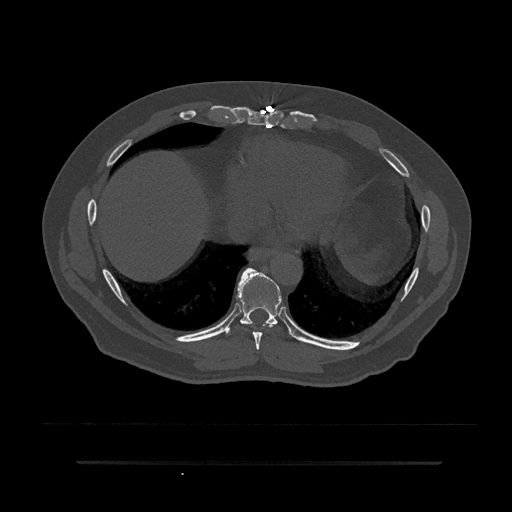
CT including the spine, one axial slice. Slice 399 of 797 in the series (ordered by position). Reconstruction kernel Br40s/3. Bone window (W 1800 / L 400 HU). 0.5 mm slice thickness. 512 × 512 image matrix. Patient: male, 59 years. From the clinical record (not read from this slice): primary cancer: bile ducts.
Annotated regions visible in this slice (semi-automatic segmentation, software-assisted and operator-edited):
- T8 vertebra: bounding box [x1, y1, x2, y2] px = [252, 325, 273, 351]
- T9 vertebra: [226, 268, 282, 334]